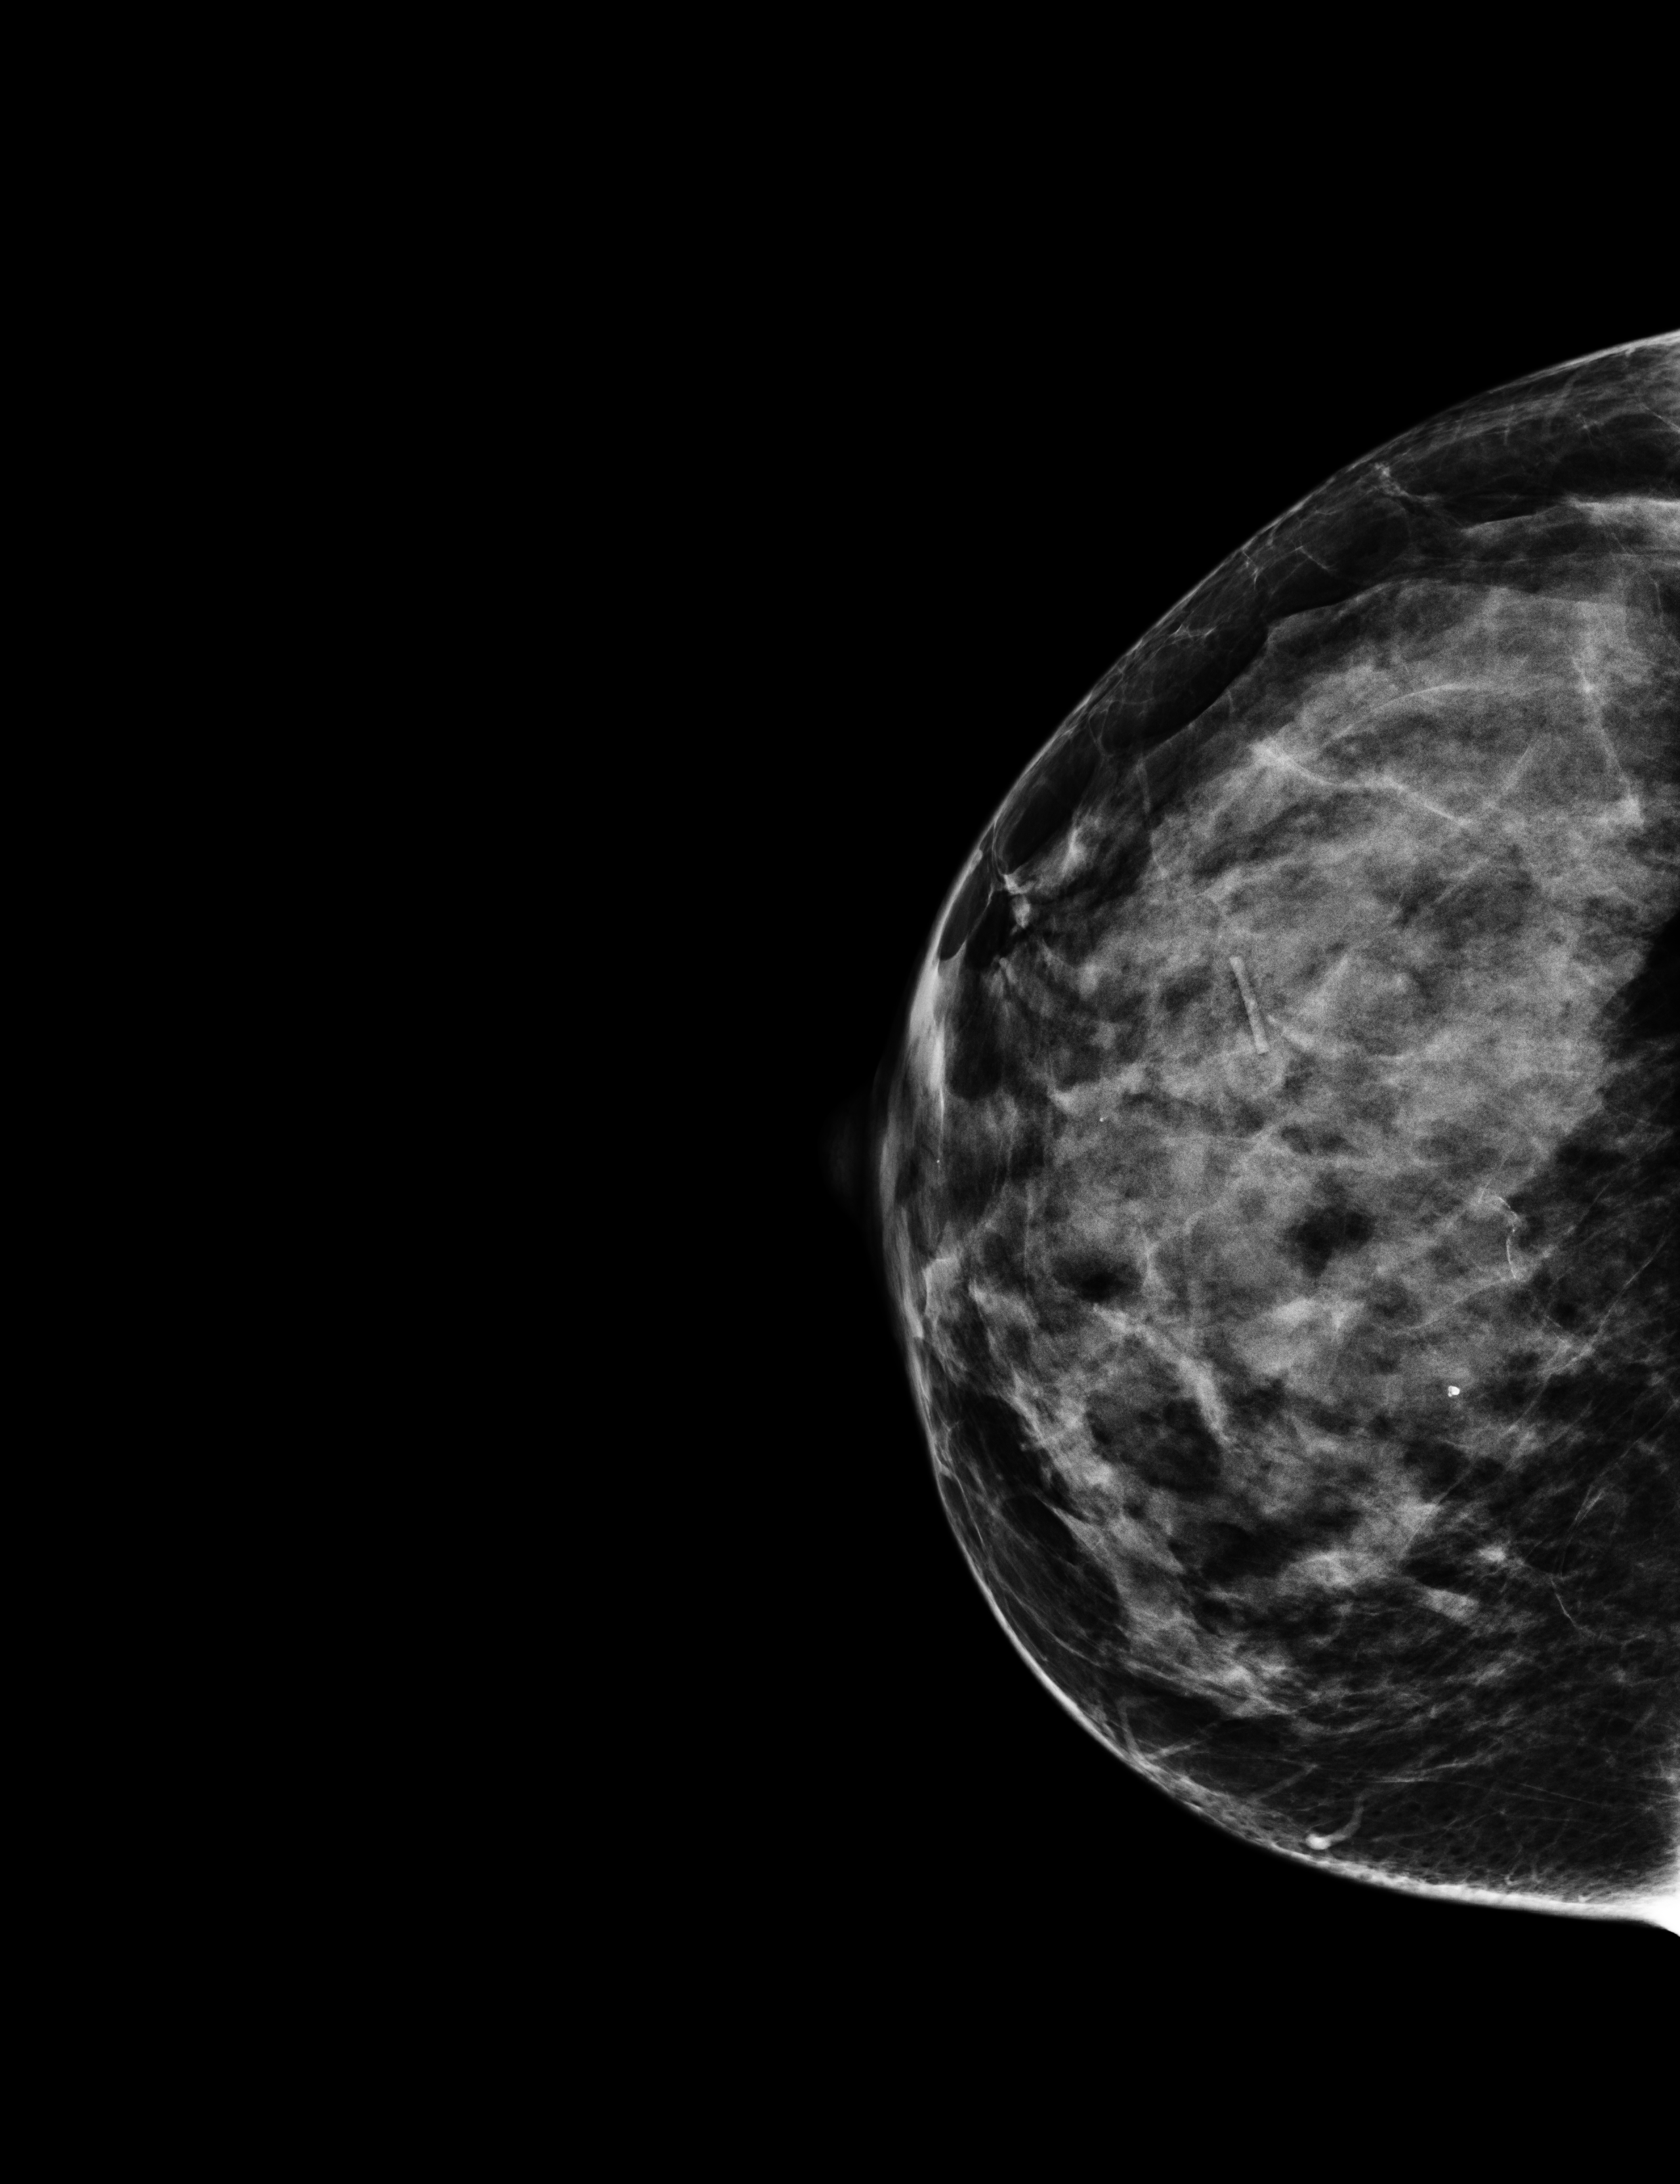
Digital mammogram (FFDM), right breast, CC view, annual screening mammography examination. Female patient, age 47 years.
- BI-RADS breast density category at the screening exam (both breasts, scale 1–4): 3
- final BI-RADS category for the screening round (tomosynthesis exam, both breasts): category 4
- recall: recalled for additional imaging after this screen